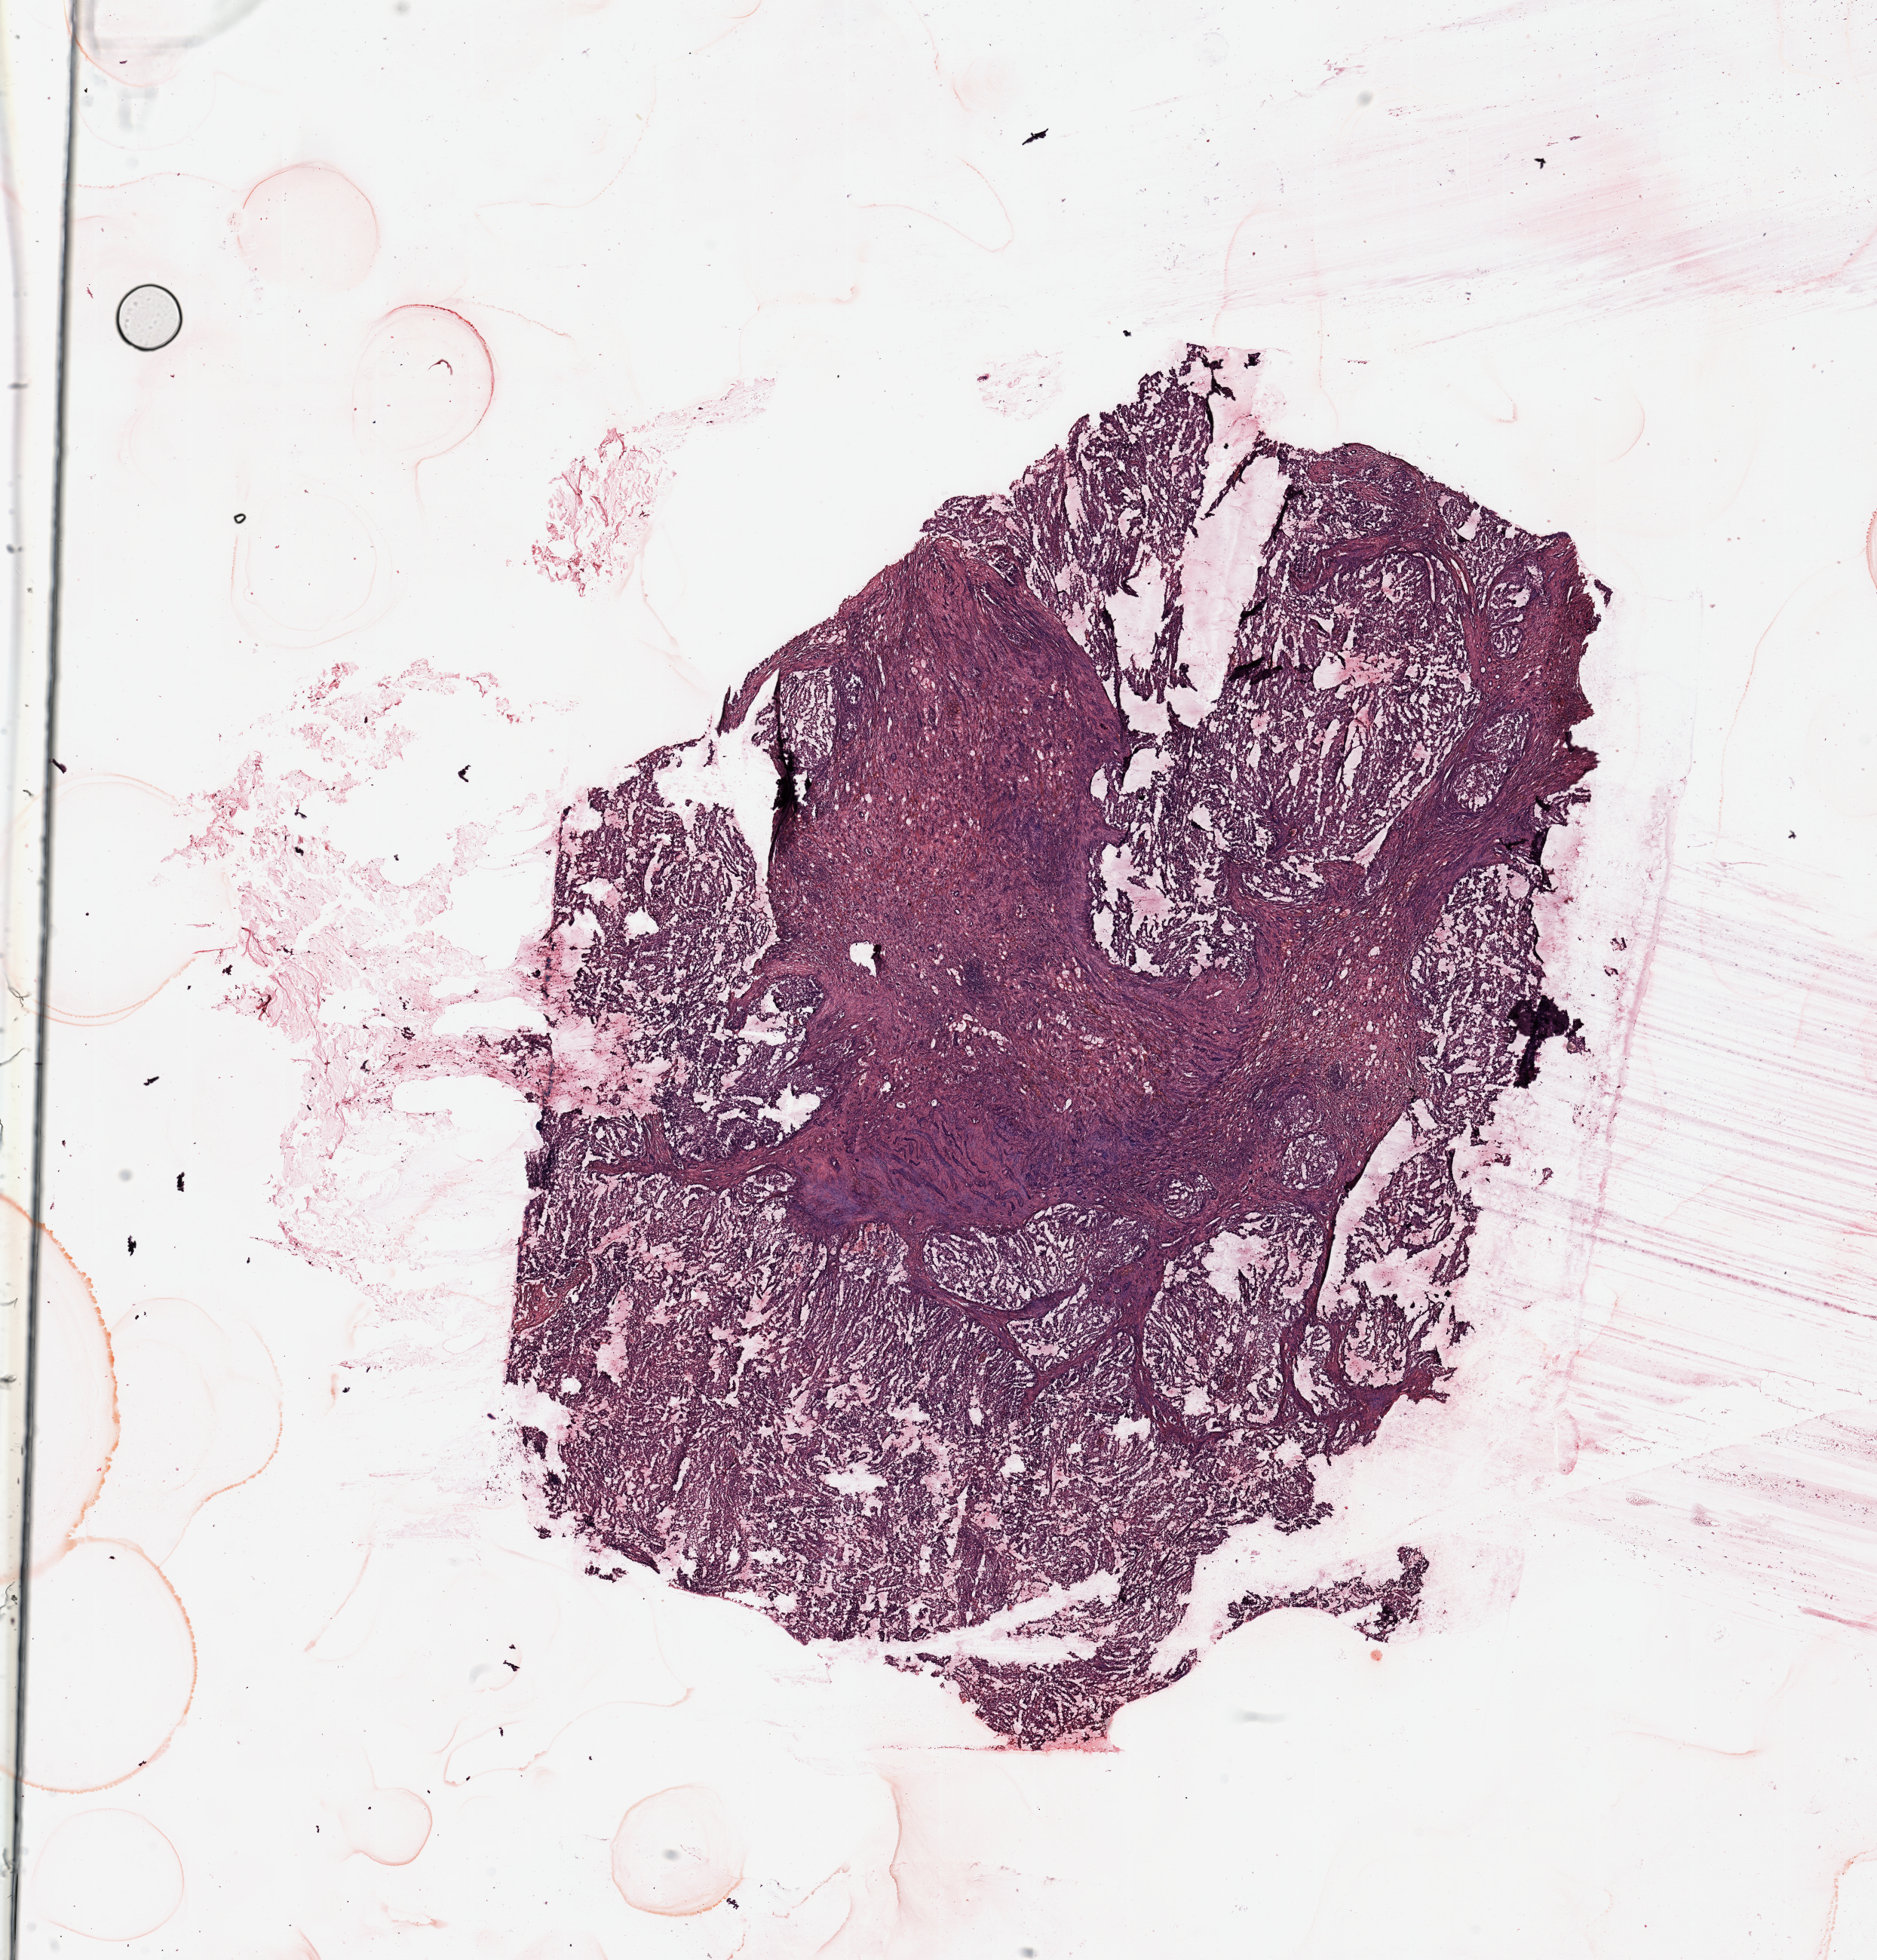
Hematoxylin and eosin (H&E) stained whole-slide image, low-resolution overview of the scanned area, about 19.7 x 20.6 mm, kidney, tumour tissue. Male, 72 y/o.
Histologic diagnosis: Renal cell carcinoma, NOS.